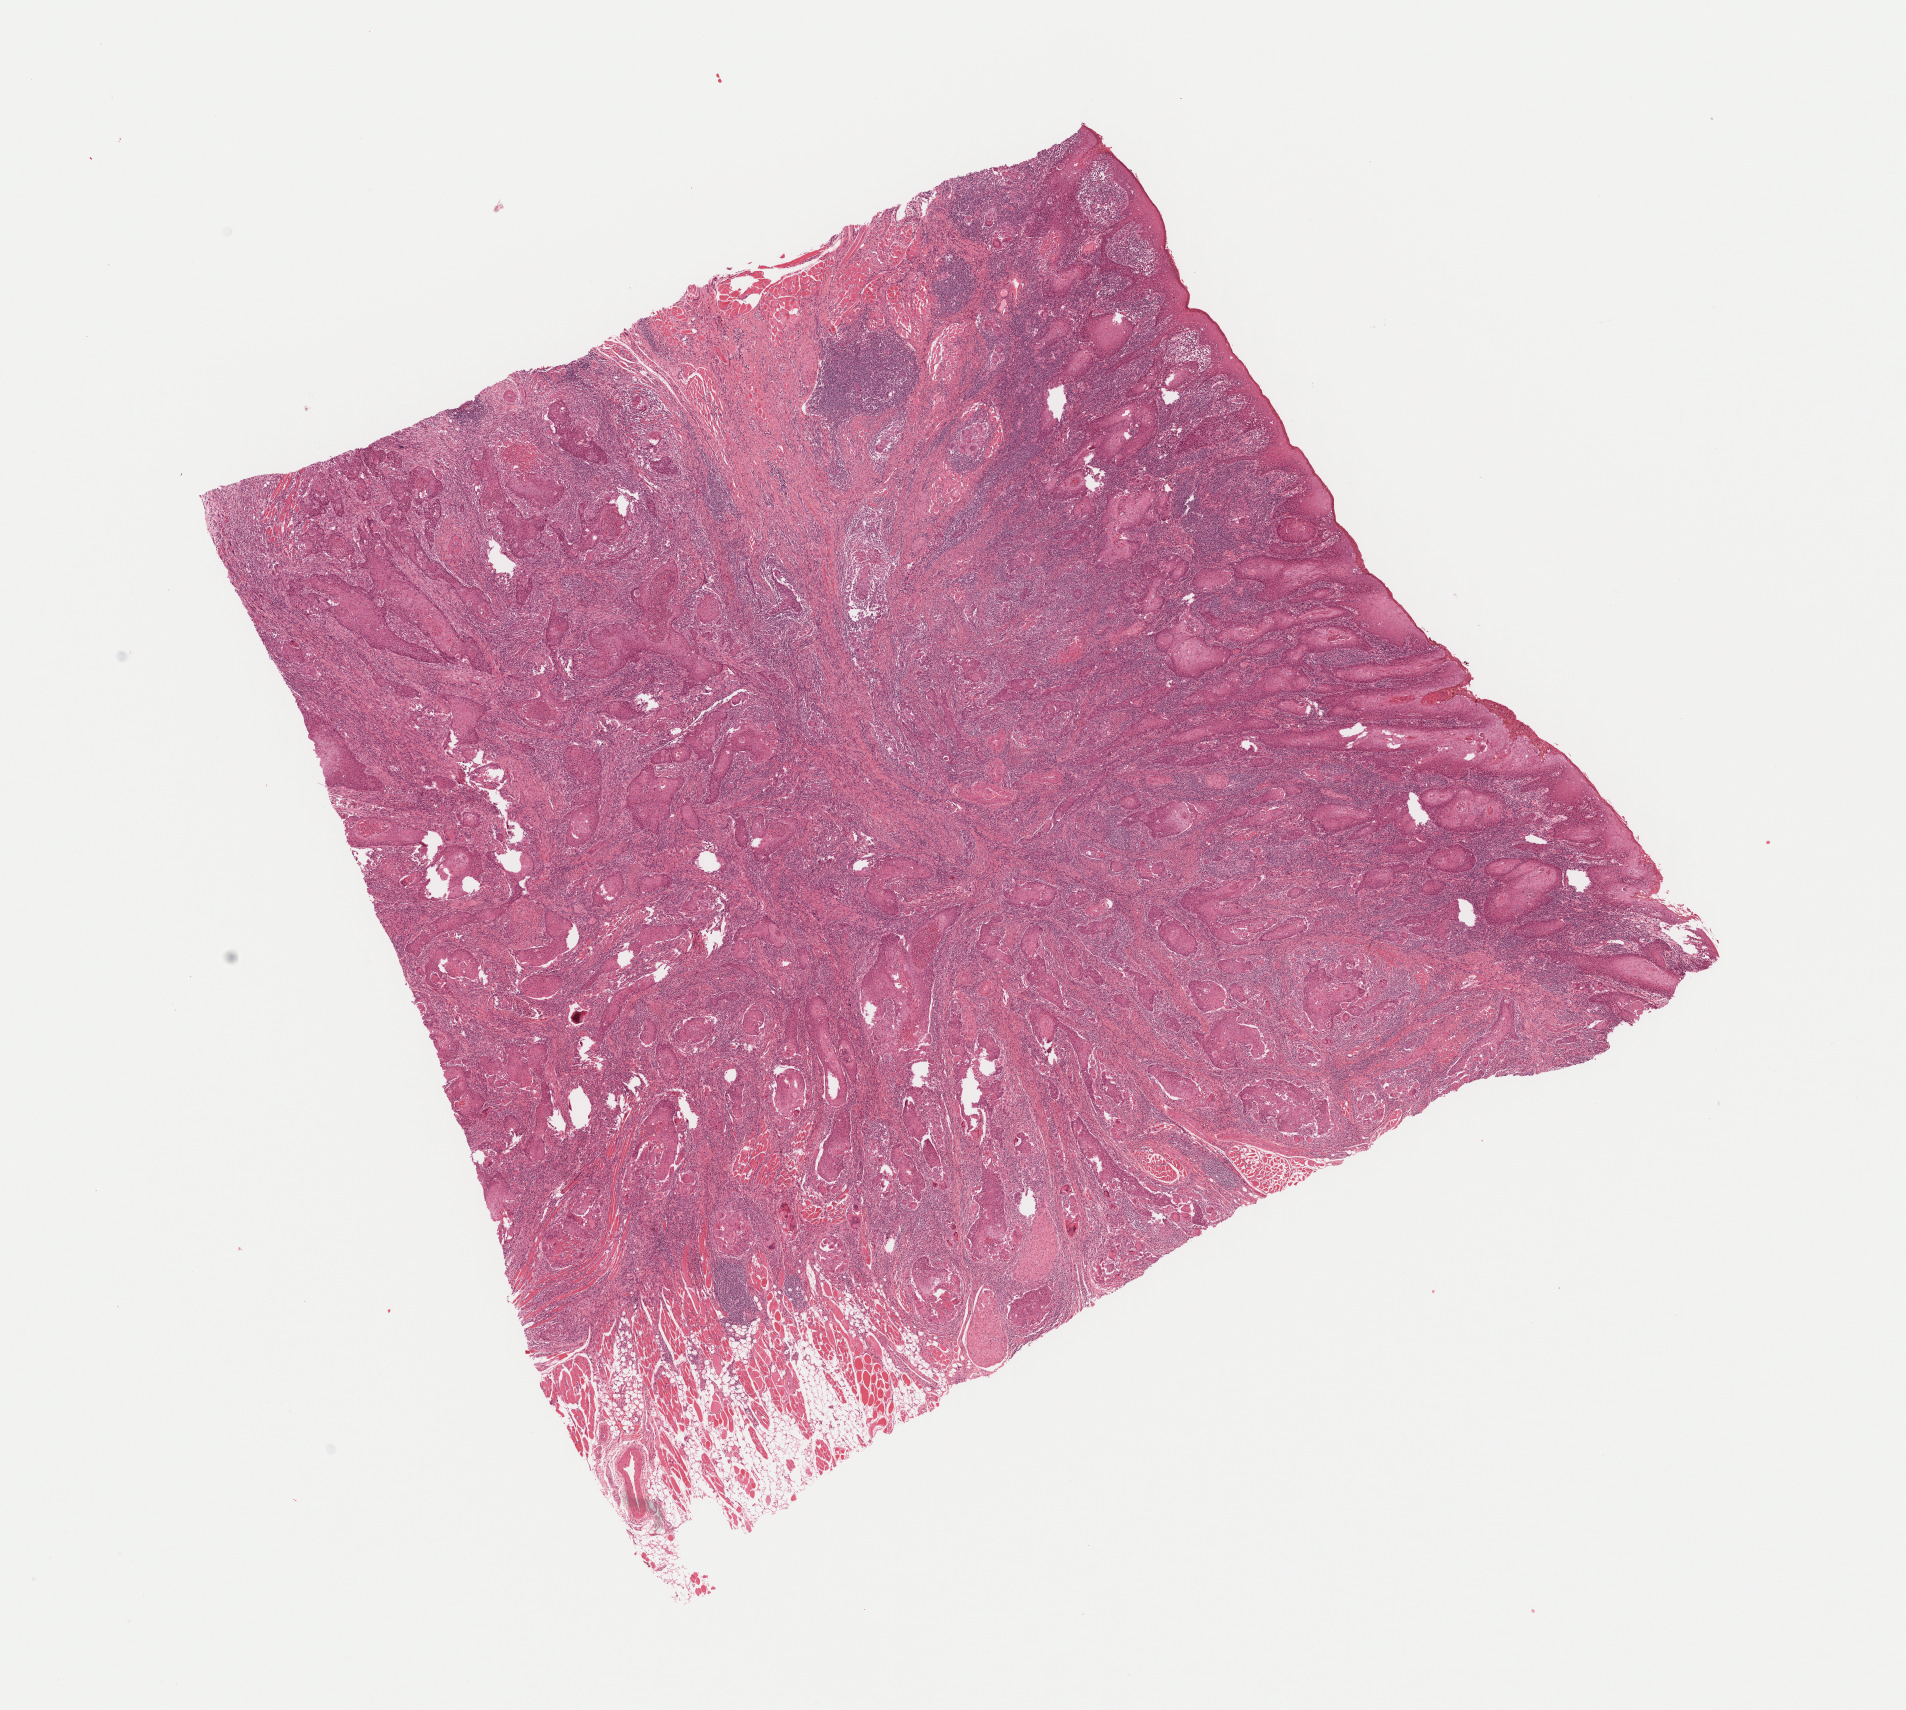
Digitized Hematoxylin and eosin (H&E) stained tissue section (whole slide), whole scanned area (about 15.4 x 13.8 mm, slide scanned at 40x) shown as a low-resolution overview. Formalin-fixed paraffin-embedded (FFPE) diagnostic section. Sample: primary tumour, head and neck. Male, age 63 years at initial diagnosis. Histologic grade: G2 (moderately differentiated).
AJCC pathologic stage: IVA (6th edition). TNM: T2 N2b. Pathologic diagnosis: Squamous cell carcinoma, NOS (tongue, NOS).